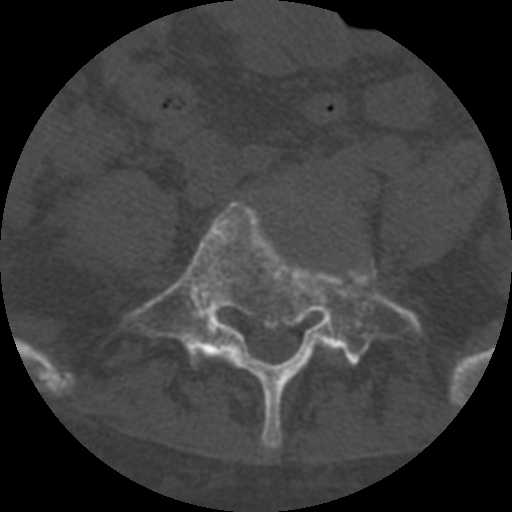
CT including the spine, one axial slice; slice 188 of 708 in the series (ordered by position); 120 kVp; one of 3 acquisitions stored at this slice position; bone window (W 1800 / L 400 HU); 1.25 mm slice thickness; 512 × 512 image matrix, field of view 160 × 160 mm. Patient age 55 years. From the clinical record (not read from this slice): primary cancer: colon.
Annotated regions visible in this slice (semi-automatic segmentation, software-assisted and operator-edited):
- L5 vertebra: bounding box [x1, y1, x2, y2] px = [122, 193, 422, 450]